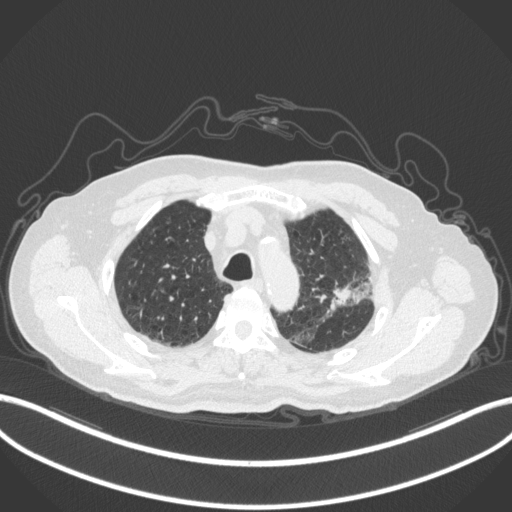
Chest CT, one axial slice; slice 239 of 331 in the series (ordered by position); 120 kVp; lung window (W 1500 / L -600 HU); 1 mm slice thickness; 512 × 512 image matrix. Patient: male, 79 years. From the clinical record (not read from this slice): clinical TNM (as recorded): T2a N1 M1.
Annotated regions visible in this slice (rectangle marked by the reading radiologist):
- lung tumour (recorded histology: adenocarcinoma): bounding box (x1, y1, x2, y2) in pixels: (324, 274, 373, 317)